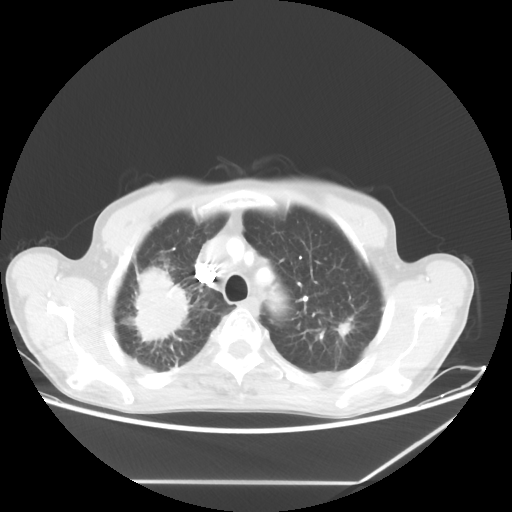
Chest CT, one axial slice; slice 51 of 65 in the series (ordered by position); reconstruction kernel STANDARD; 80 kVp; lung window (W 1500 / L -600 HU); 5 mm slice thickness; 512 × 512 image matrix. Male patient, age 68 years. From the clinical record (not read from this slice): clinical TNM (as recorded): T3 N3 M0.
Annotated regions visible in this slice (bounding box drawn by a radiologist):
- lung tumour (recorded histology: adenocarcinoma): box from (x=119, y=265) to (x=194, y=350) px